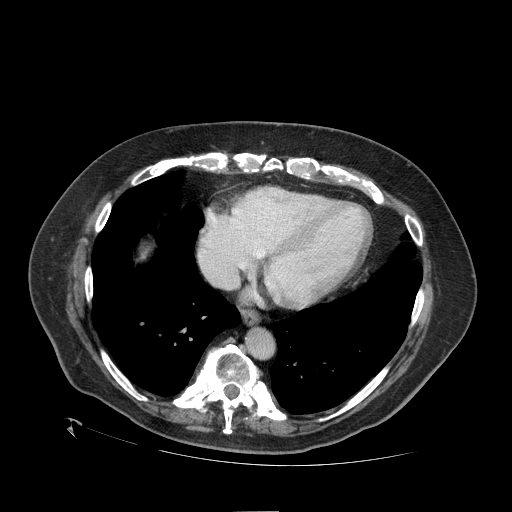
Contrast-enhanced abdominal CT (liver protocol), one axial slice; position 101 of 109 along the scan axis; reconstruction kernel STANDARD; one of 2 acquisitions stored at this slice position; soft-tissue window (W 400 / L 40 HU); 2.5 mm slice thickness; 512 × 512 image matrix, field of view 460 × 460 mm. From the clinical record (not read from this slice): diagnosis: hepatocellular carcinoma (patient treated with transarterial chemoembolisation; whether this scan precedes or follows treatment is not stated here); TNM stage (as recorded): Stage-I; Child-Pugh class: A; tumour nodularity: uninodular; tumour size: 4.6 cm.
Annotated regions visible in this slice (semi-automatic segmentation, software-assisted and operator-edited):
- liver parenchyma outside the tumour (the mass and vessels are separate outlines, so this box may not span the whole liver): bounding box <140,244,150,258> (left, top, right, bottom; pixels)